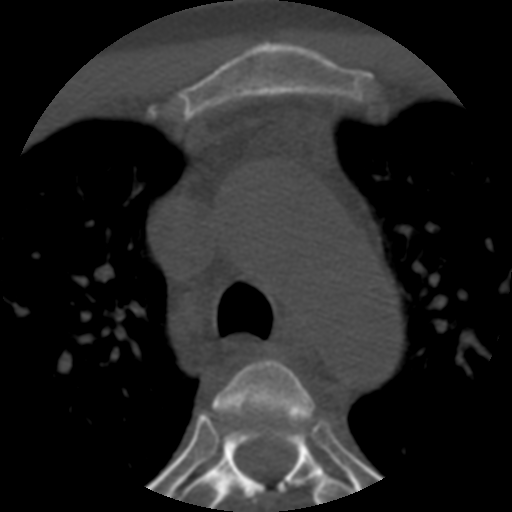
CT including the spine, one axial slice. Slice 403 of 508 in the series (ordered by position). Bone window (W 1800 / L 400 HU). 512 × 512 image matrix, field of view 160 × 160 mm. Patient age 57 years. From the clinical record (not read from this slice): primary cancer: prostate.
Structures marked on this image (semi-automatically segmented with operator editing):
- T3 vertebra: bounding box (x1, y1, x2, y2) in pixels: (213, 359, 314, 503)
- T4 vertebra: (178, 424, 358, 512)